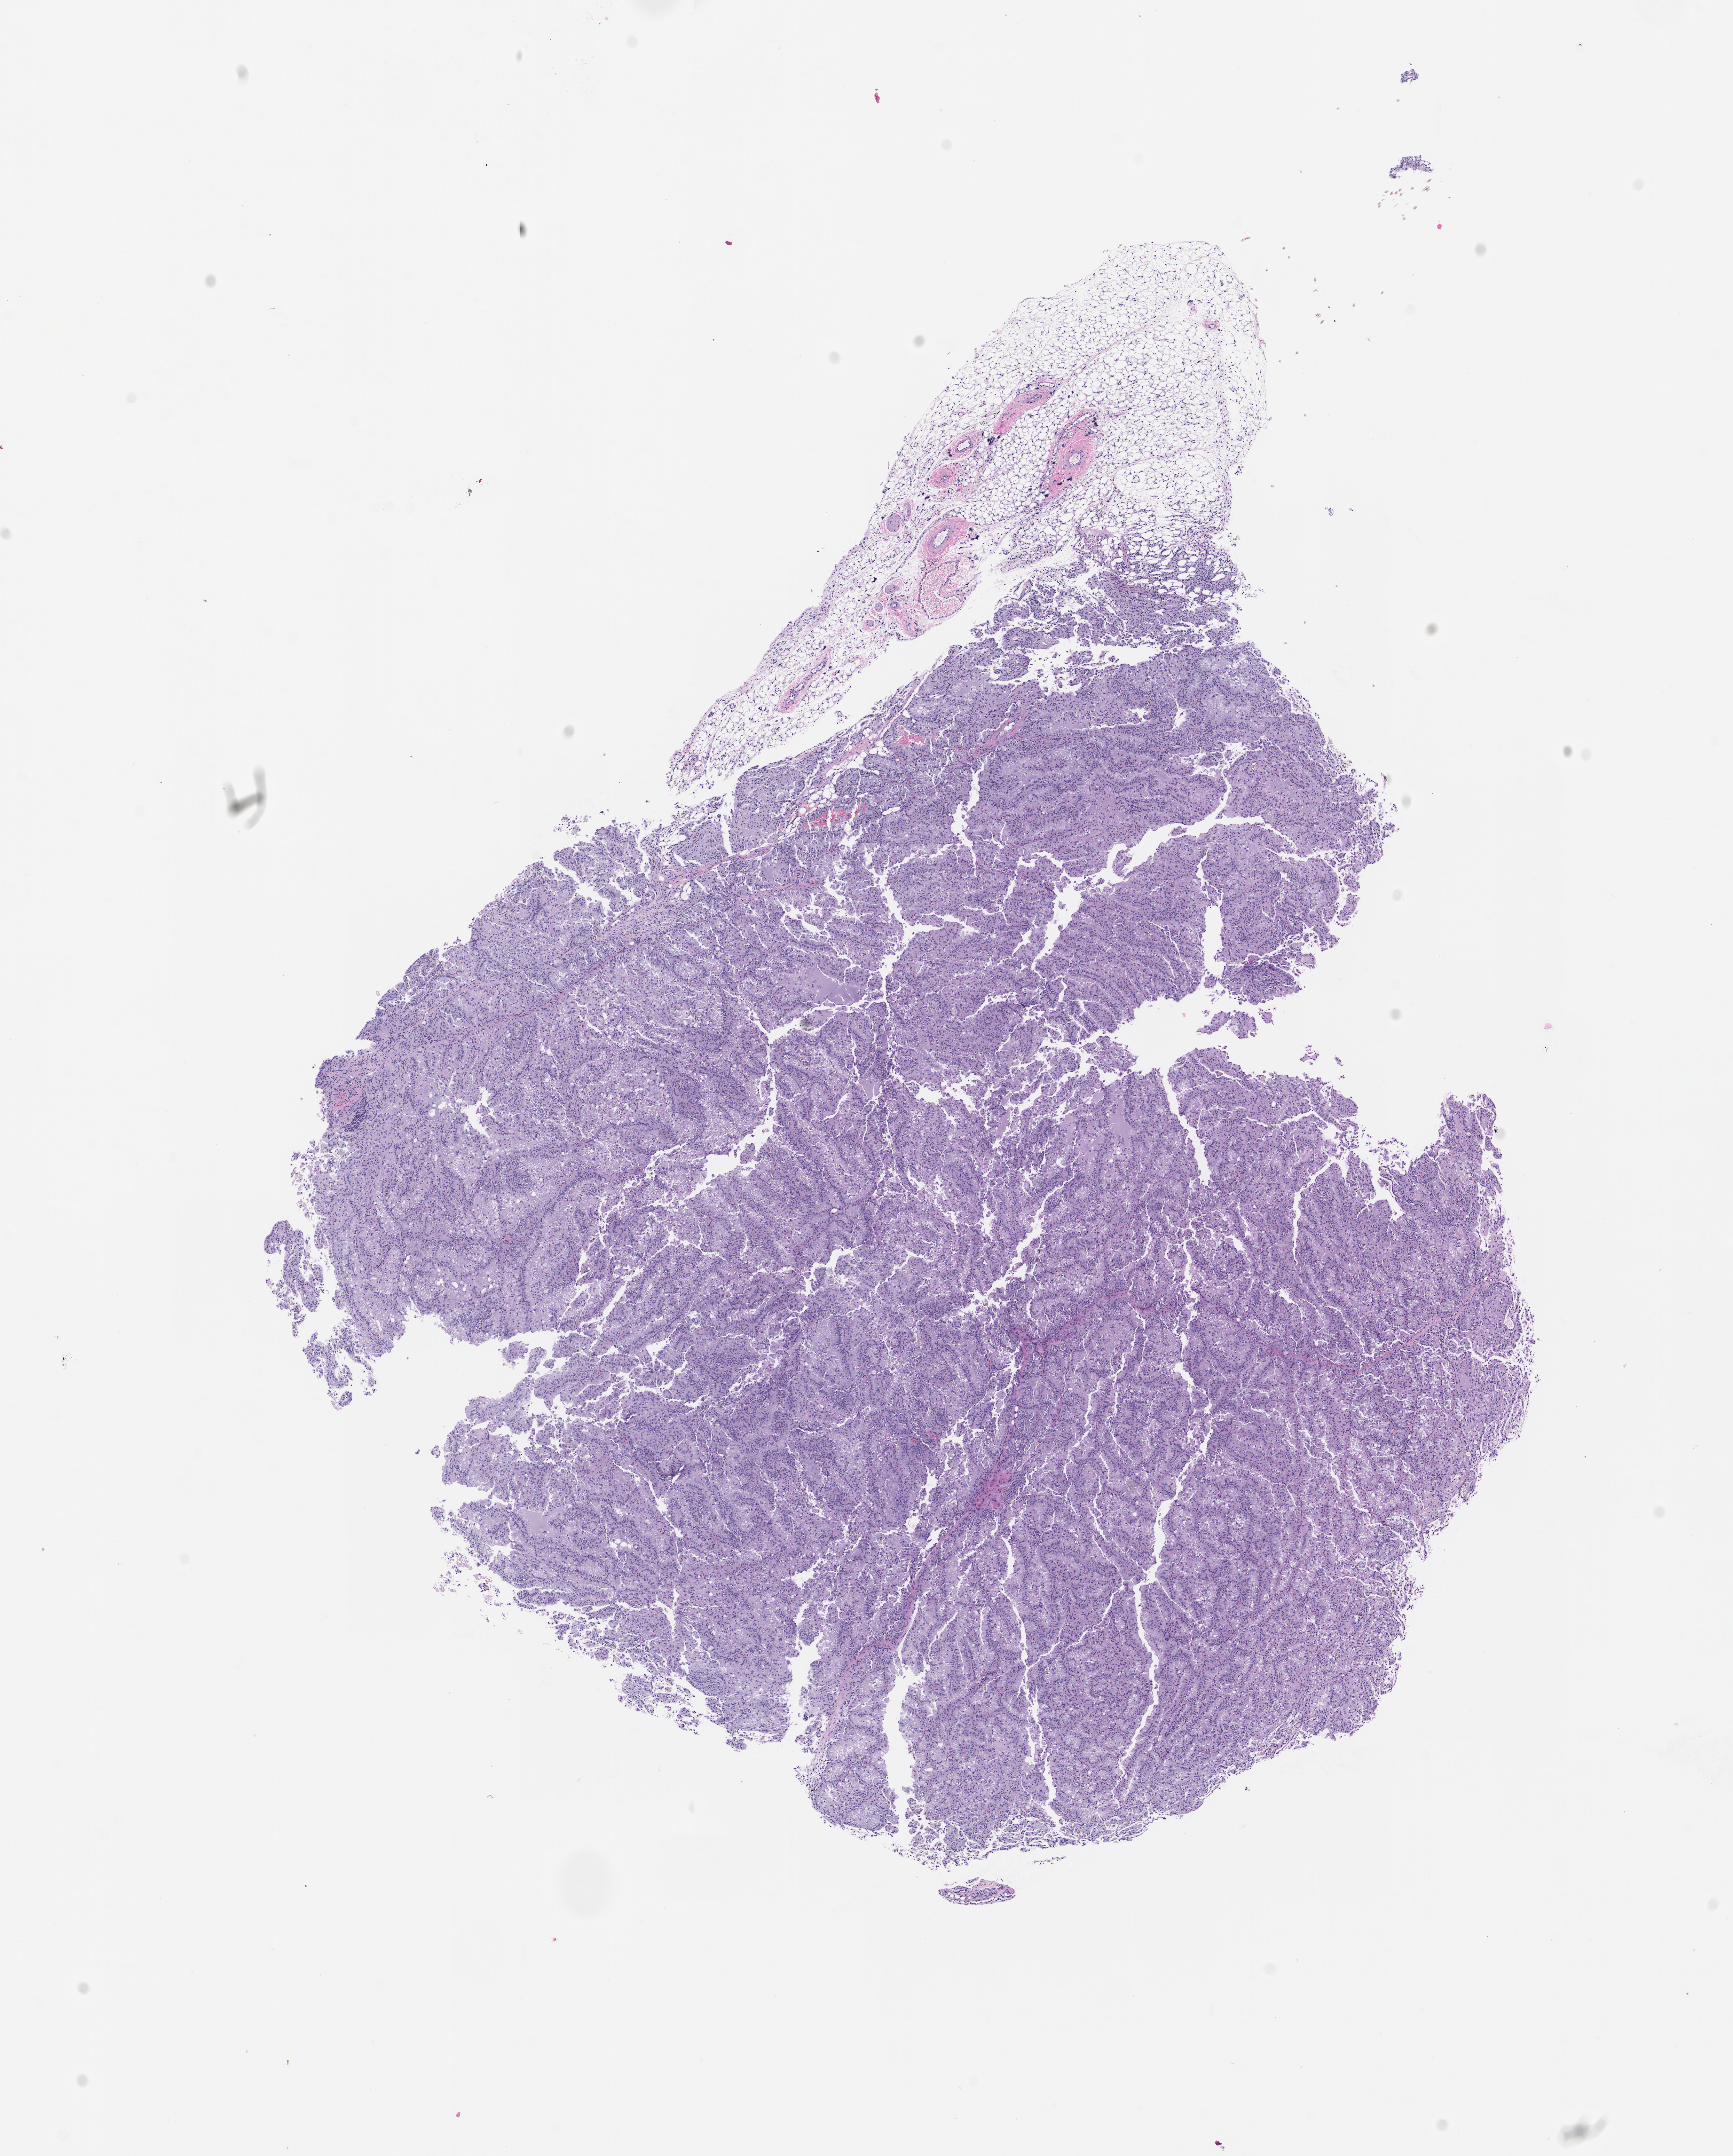
Haematoxylin and eosin whole-slide image of a patient-derived xenograft (PDX) tumor grown in a mouse, passage 0, whole scanned area (about 10.0 x 12.4 mm) shown as a low-resolution overview, FFPE section, originating tumor site category: genitourinary tract.
Originating patient diagnosis: Renal Cell Carcinoma, Not Otherwise Specified.